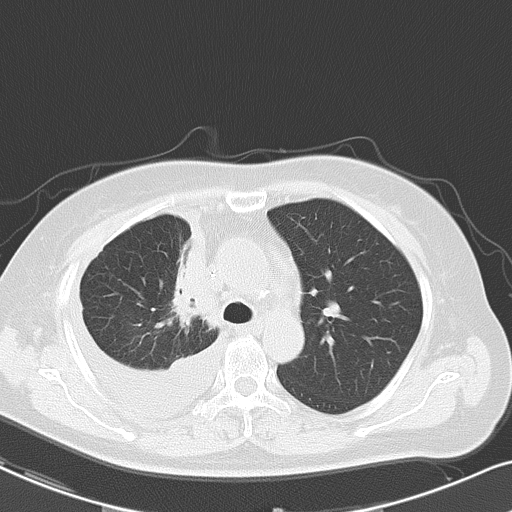
Chest CT, one axial slice; position 35 of 48 along the scan axis; reconstruction kernel B70f; lung window (W 1500 / L -600 HU); 5 mm slice thickness; 512 × 512 image matrix, field of view 328 × 328 mm. Patient: female, 69 years. From the clinical record (not read from this slice): clinical TNM (as recorded): T2a N0 M1c.
Outlined on this slice (bounding box drawn by a radiologist):
- lung tumour (recorded histology: adenocarcinoma): bounding box (x1, y1, x2, y2) in pixels: (168, 208, 218, 336)